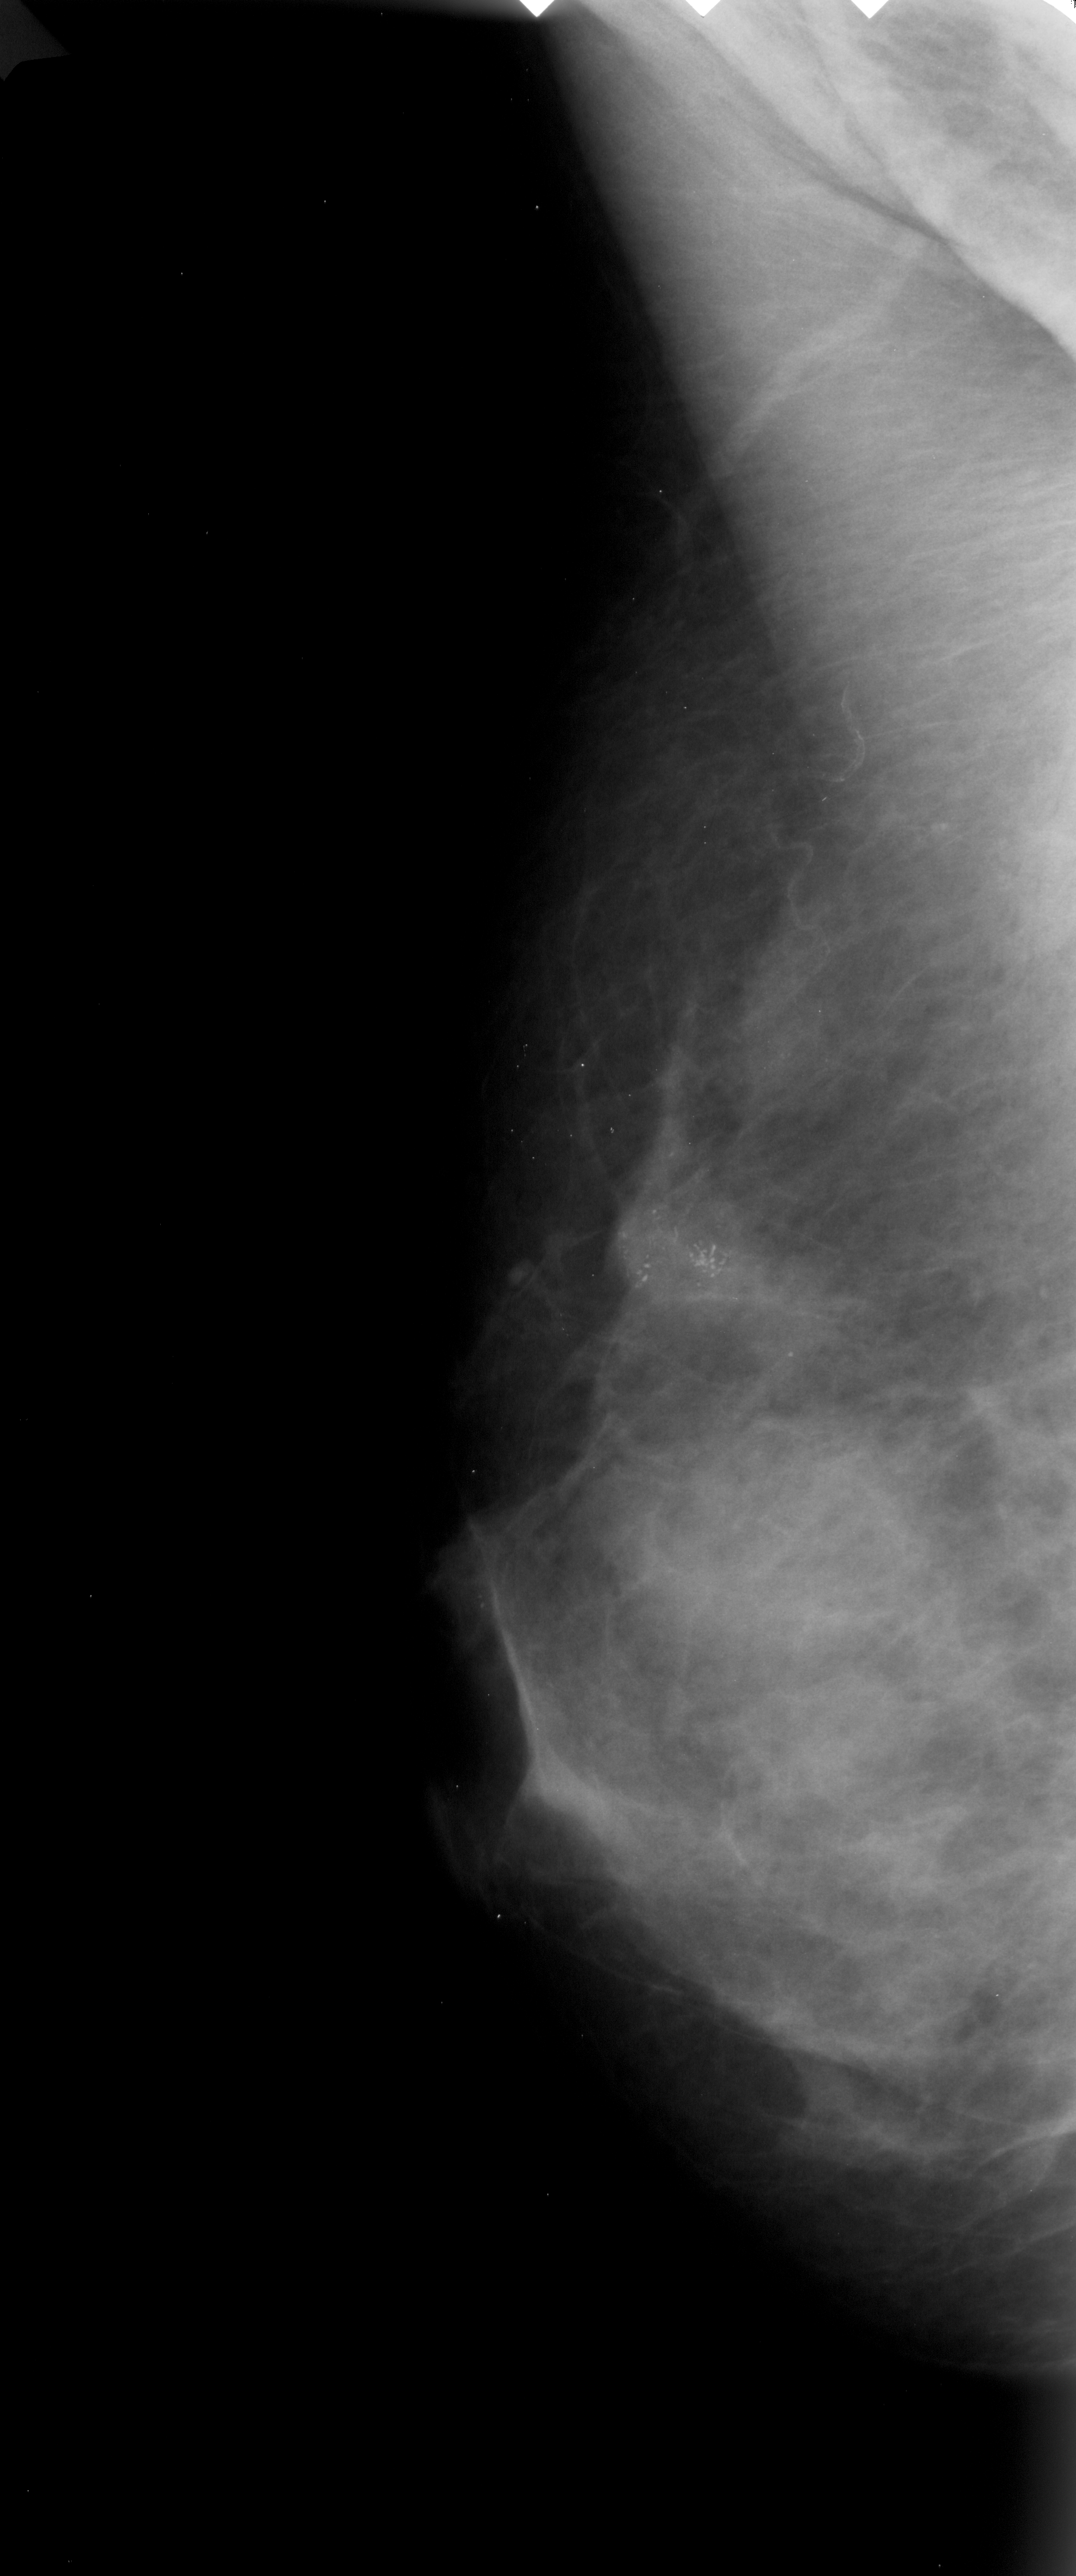
Scanned film-screen mammogram; left breast; MLO view.
- Abnormality record for this image: calcifications, morphology pleomorphic, distribution clustered; BI-RADS assessment category 4; subtlety rating 5 on a 1 (subtle) to 5 (obvious) scale; pathology result (as recorded, not read from the image): malignant.